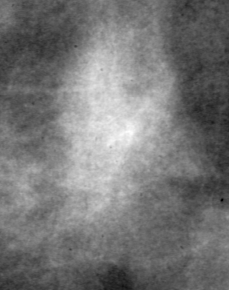
Region of interest cut from a scanned film mammogram (one marked finding), left breast, MLO view.
Mass, shape irregular, margins ill defined; BI-RADS assessment category 4; subtlety rating 3 on a 1 (subtle) to 5 (obvious) scale; pathology result (as recorded, not read from the image): benign.